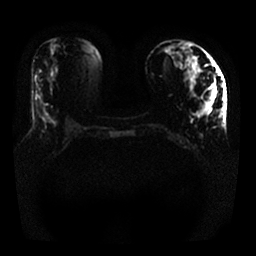
Breast MRI, one axial slice. Diffusion-weighted series; image 2 of 4 stored at this slice position (different b-values; order by instance number). 1.5 T. 4 mm slice thickness. 256 × 256 image matrix, field of view 340 × 340 mm. Female patient.
Annotated regions visible in this slice (manually delineated by an expert):
- tumour on diffusion-weighted imaging: bounding box <203,85,216,114> (left, top, right, bottom; pixels)